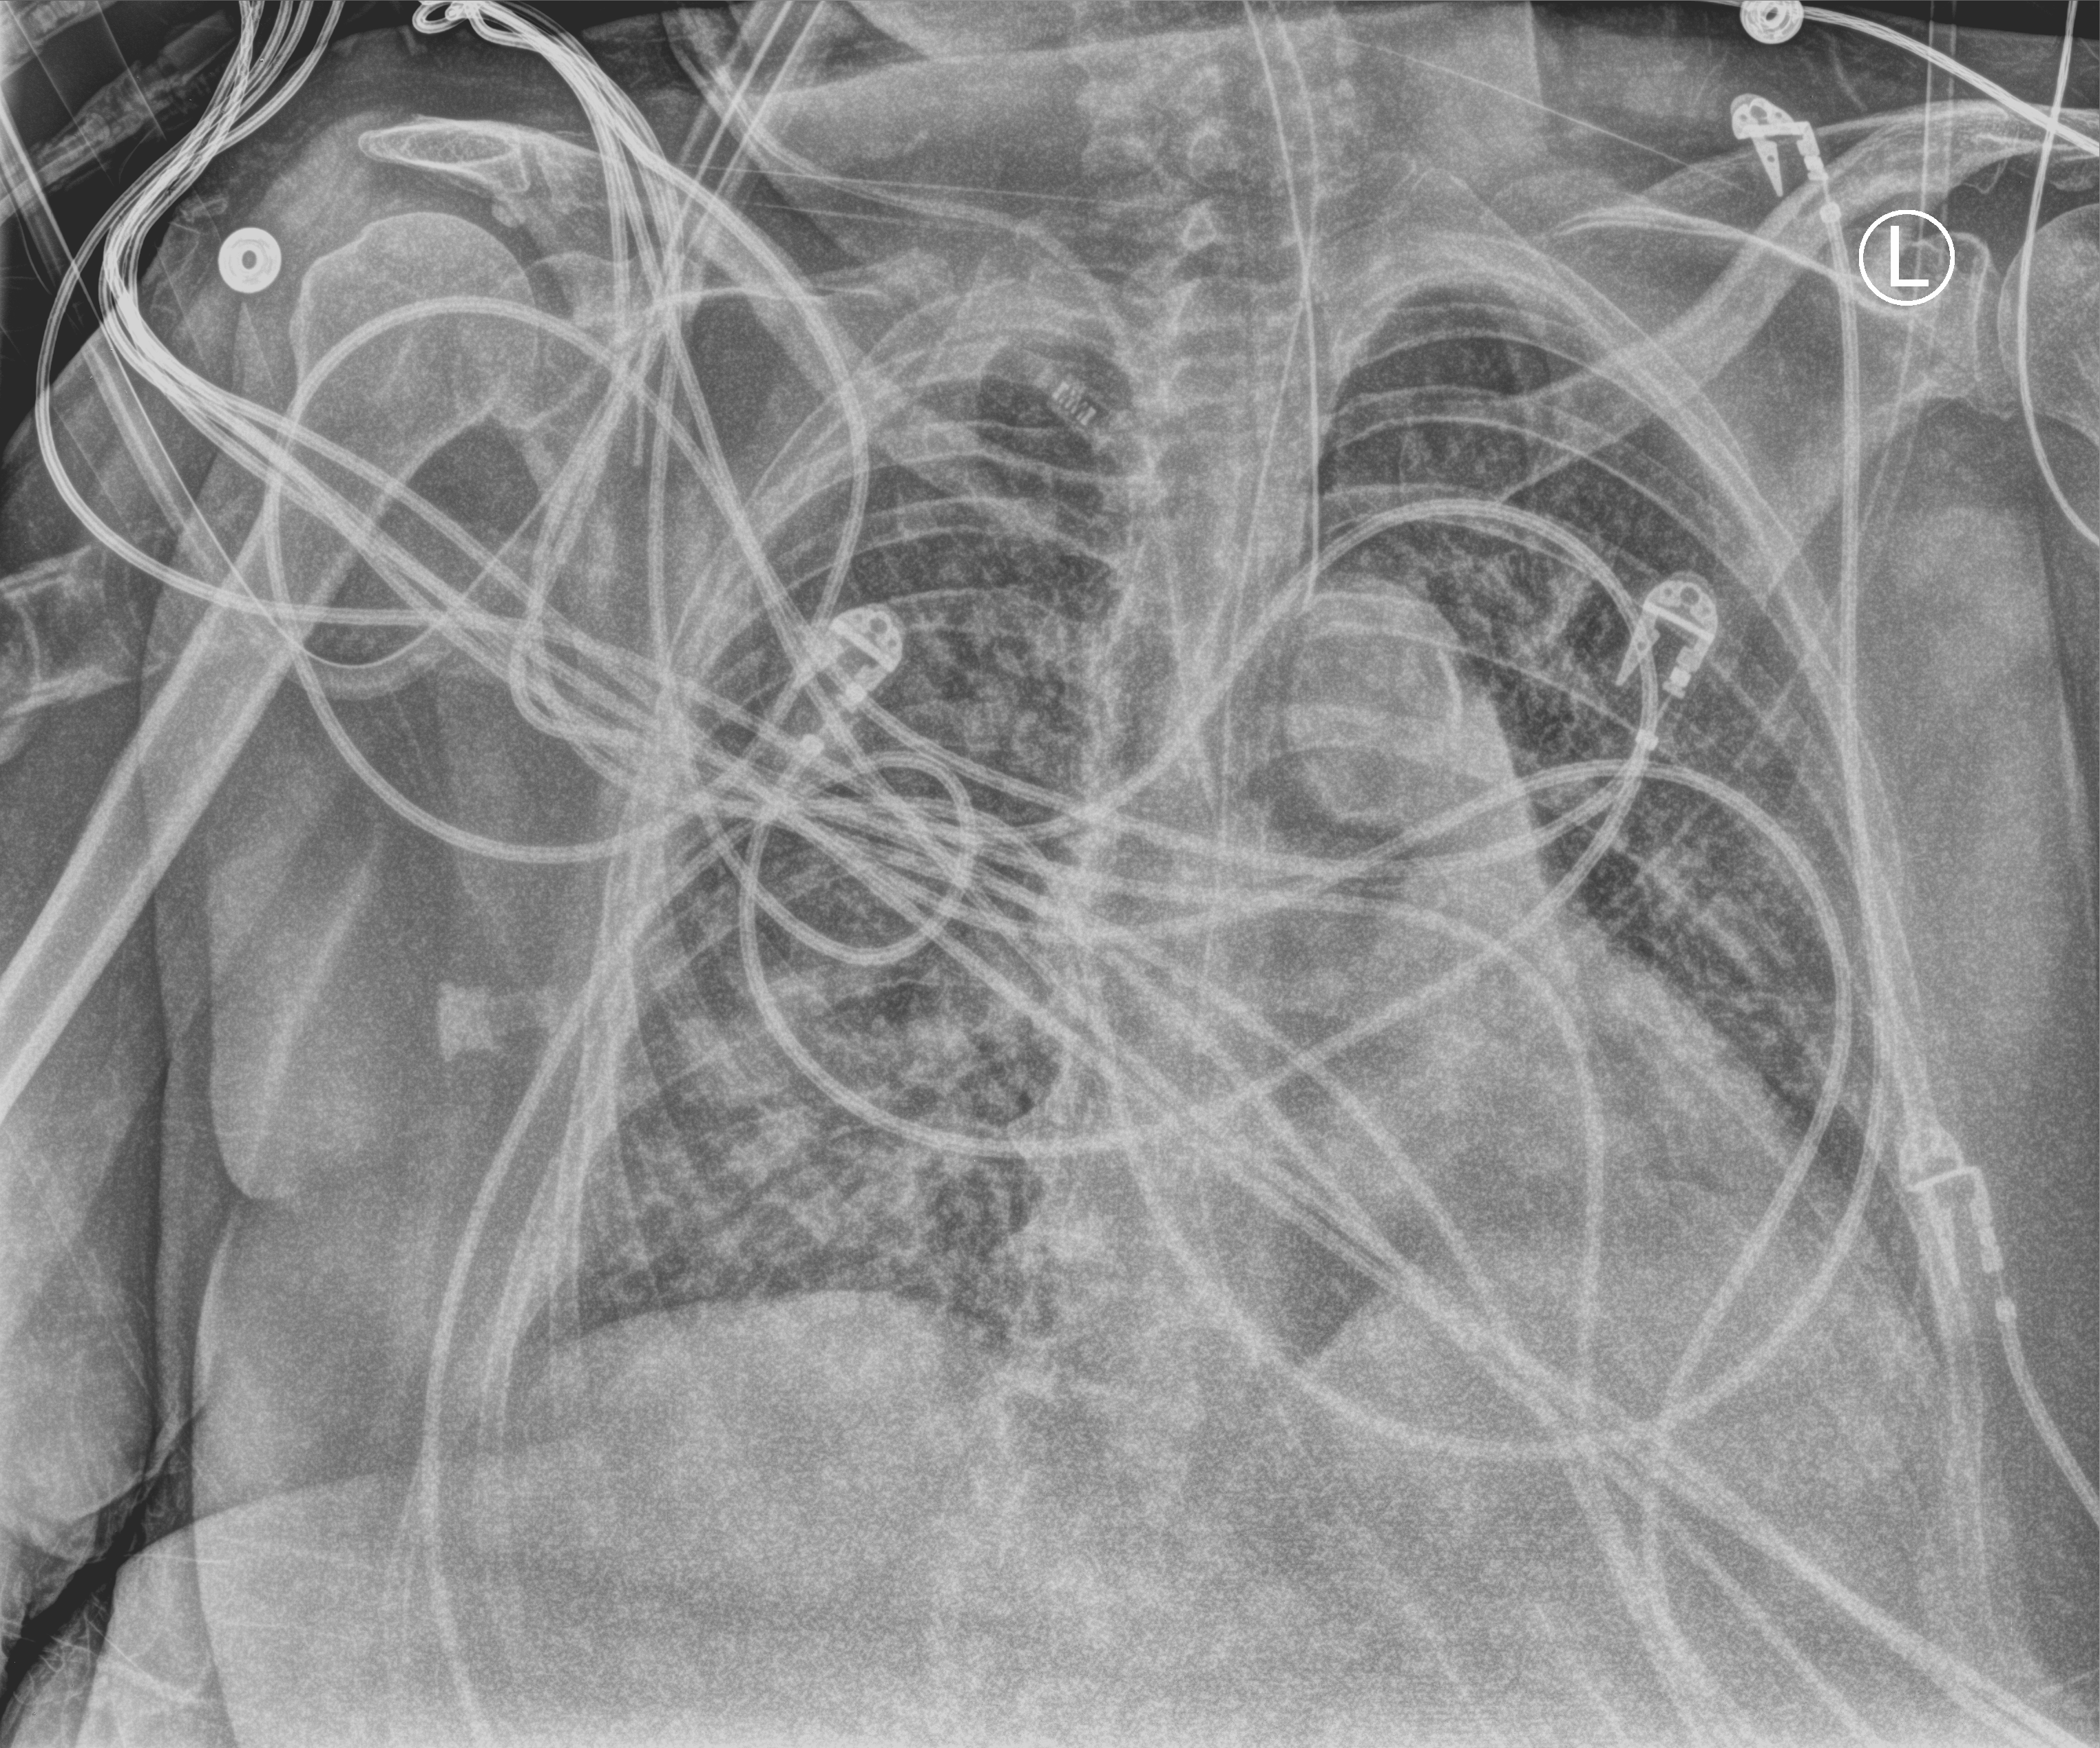
Chest X-ray (portable); anteroposterior (AP) projection. Patient hospitalised with COVID-19; female, aged 75–90 years.
Admission-level facts for this patient (not findings on this image; timing relative to this image not recorded):
- mechanically ventilated during this hospital stay: yes